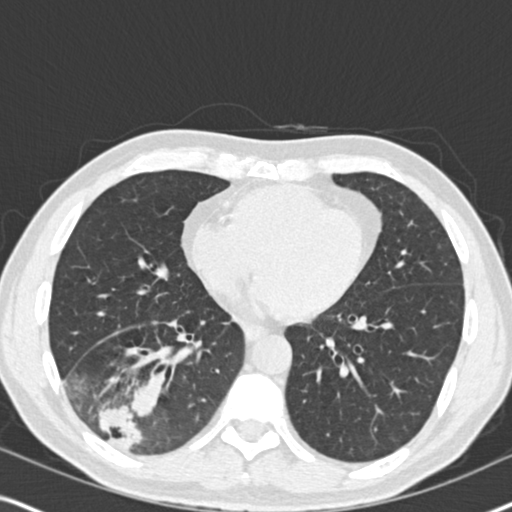
Low-dose screening chest CT, axial slice. Second annual screen. Lung window (W 1500 / L -600 HU). 120 kVp. Male participant, aged 61 years at enrolment. Current smoker at enrolment.
• Expert-annotated lung lesion, box from (x=55, y=334) to (x=191, y=466) px.
• Reader record for this screening exam (exam-level; its link to the box is not recorded): non-calcified nodule or mass ≥4 mm, right lower lobe, 90 × 80 mm, soft tissue attenuation, pre-existing on the prior screen: yes; interval growth: yes.
• Official screen result: positive, other.
• Lung cancer was diagnosed 20 days after this screen: bronchiolo-alveolar adenocarcinoma, NOS, right lower lobe, moderately differentiated (G2), stage IIIB (AJCC 6th edition), 90 mm at pathology.